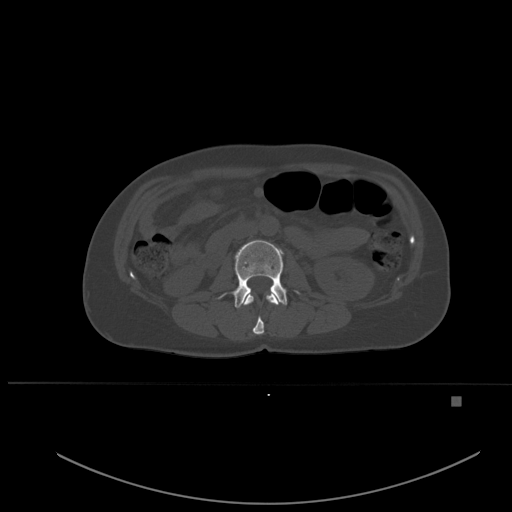
CT including the spine, one axial slice. Slice 219 of 651 in the series (ordered by position). Bone window (W 1800 / L 400 HU). 1.5 mm slice thickness. 512 × 512 image matrix, field of view 443 × 443 mm. Patient: female, 49 years. From the clinical record (not read from this slice): primary cancer: breast.
Annotated regions visible in this slice (semi-automatic segmentation, software-assisted and operator-edited):
- L1 vertebra: box from (x=243, y=293) to (x=278, y=335) px
- L2 vertebra: (x=219, y=240)–(x=299, y=308)